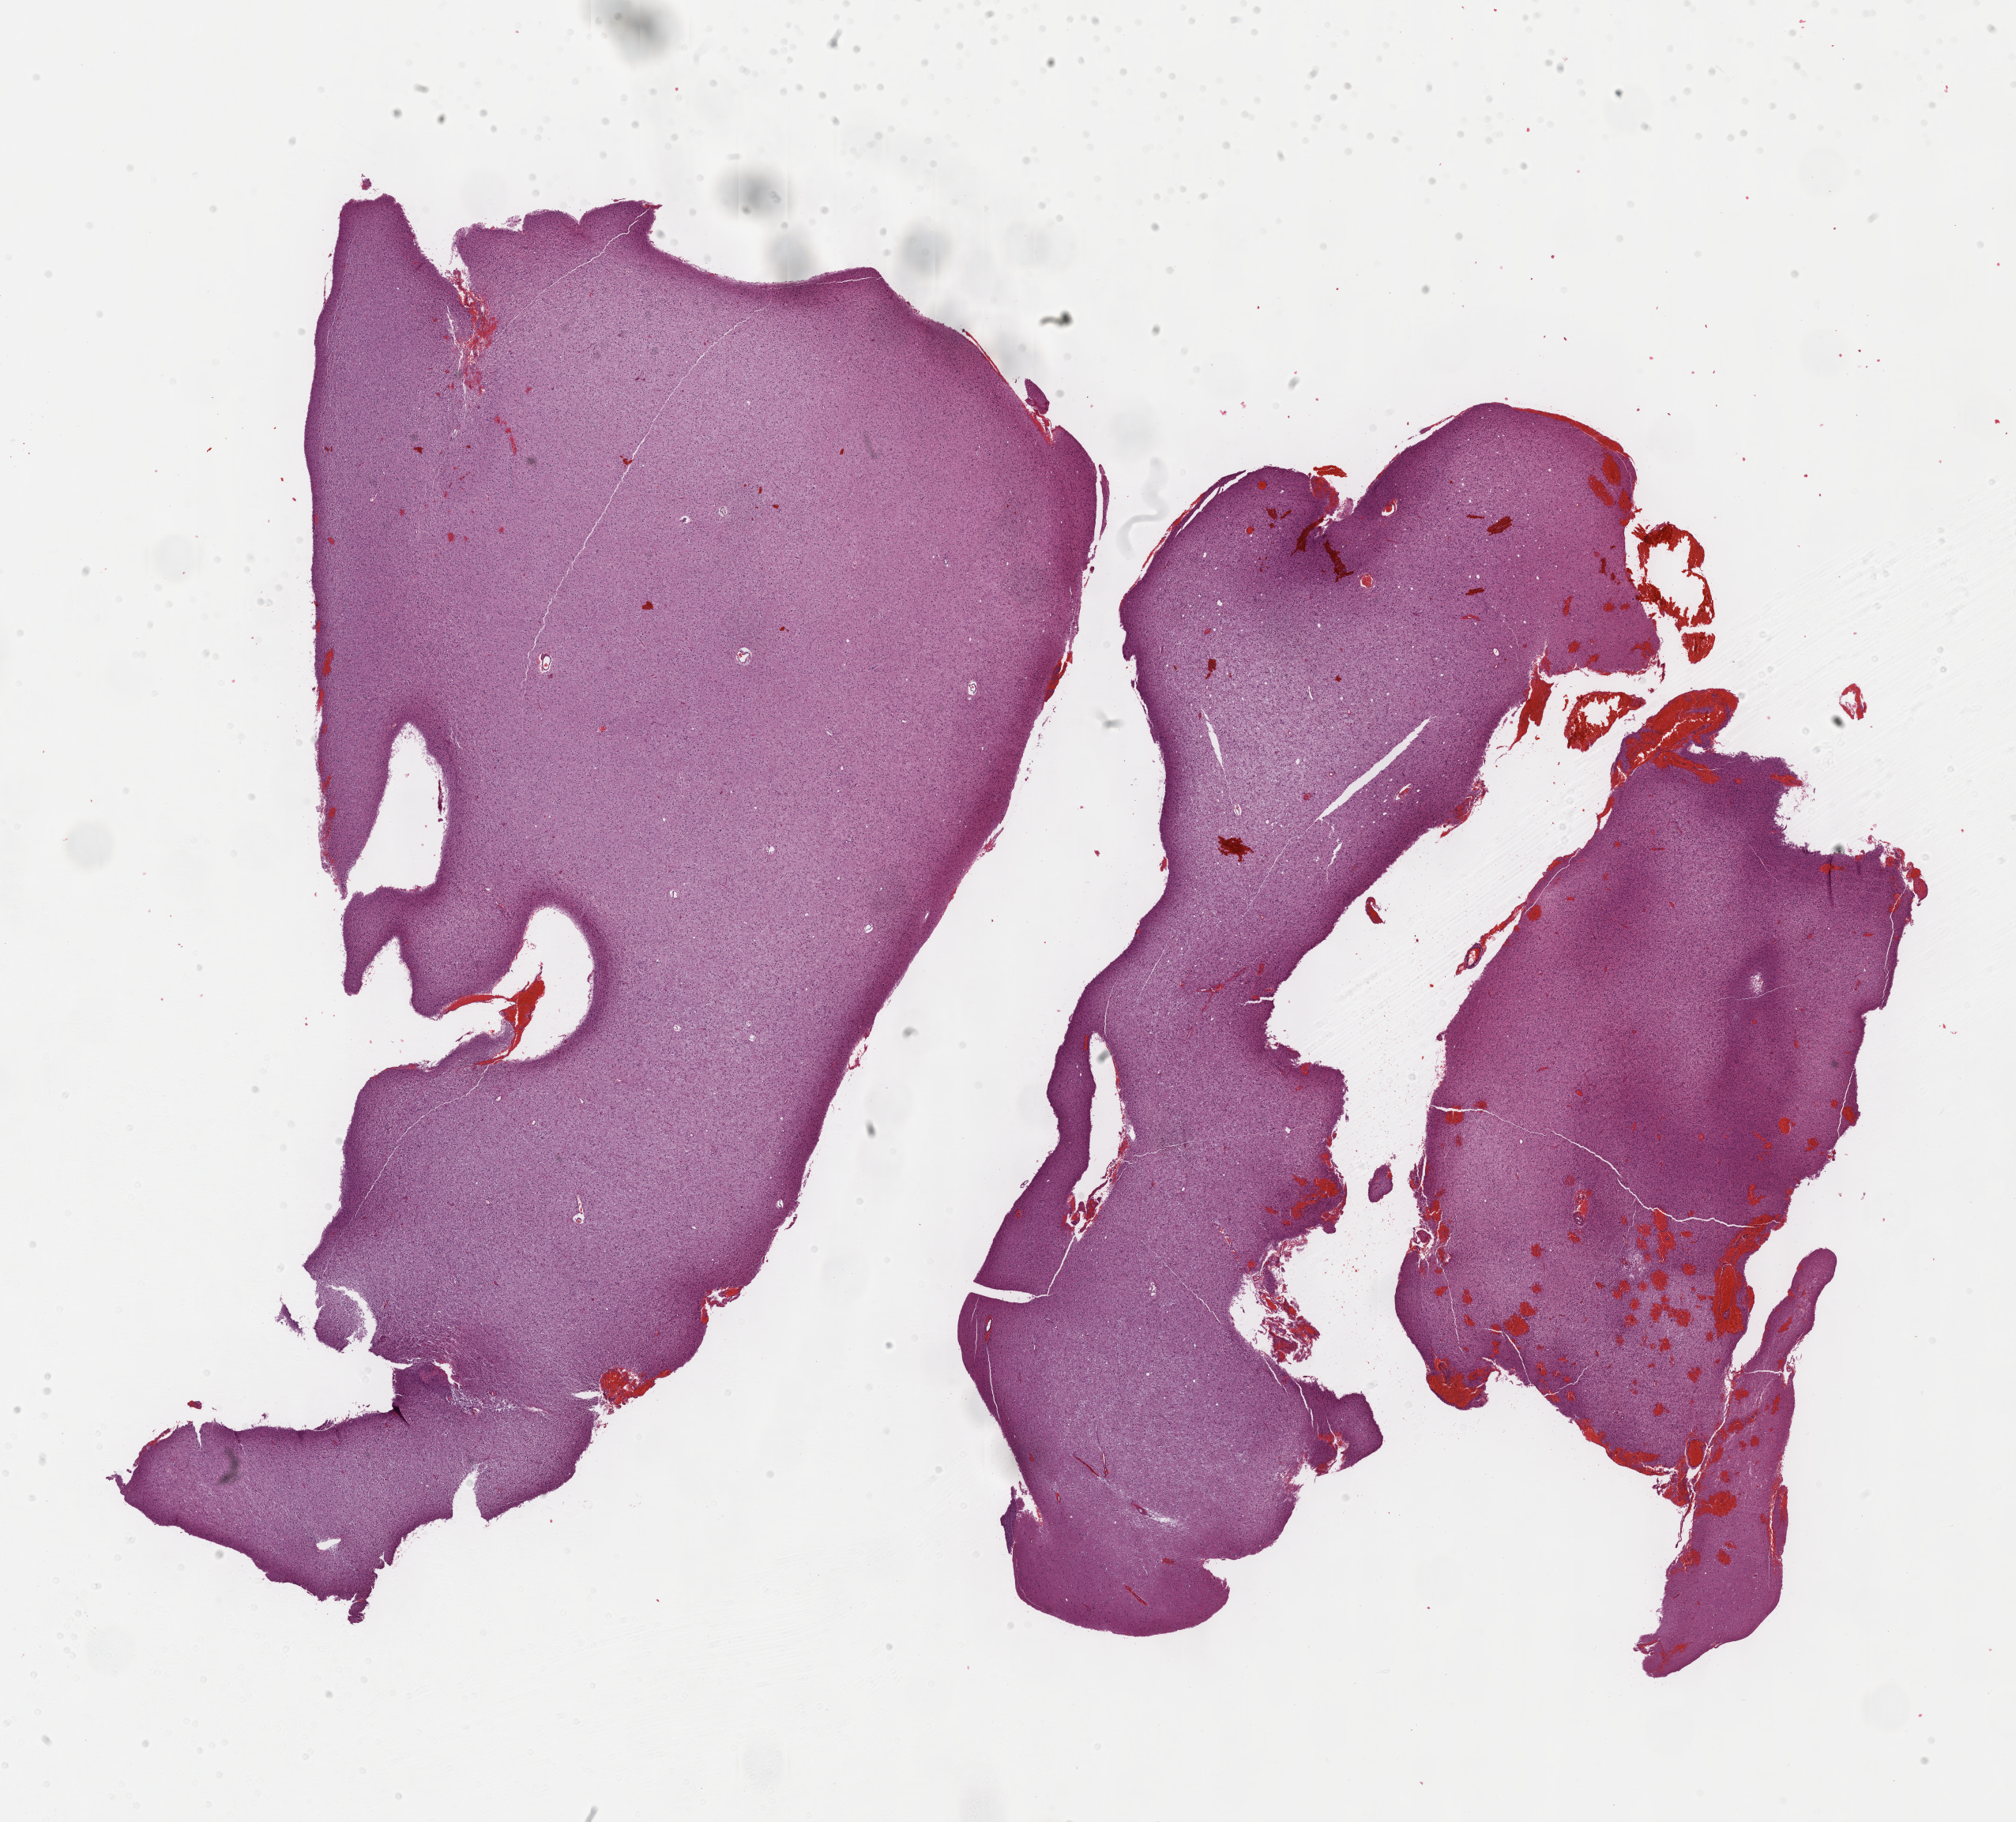
Digitized H&E tissue section (whole slide), whole scanned area (about 20.6 x 18.7 mm, slide scanned at 40x) shown as a low-resolution overview; formalin-fixed paraffin-embedded (FFPE) diagnostic section; sample: primary tumour, brain. Female patient; age at initial diagnosis 18 years. Histologic grade: G2 (moderately differentiated).
- diagnosis: Mixed glioma
- laterality: left